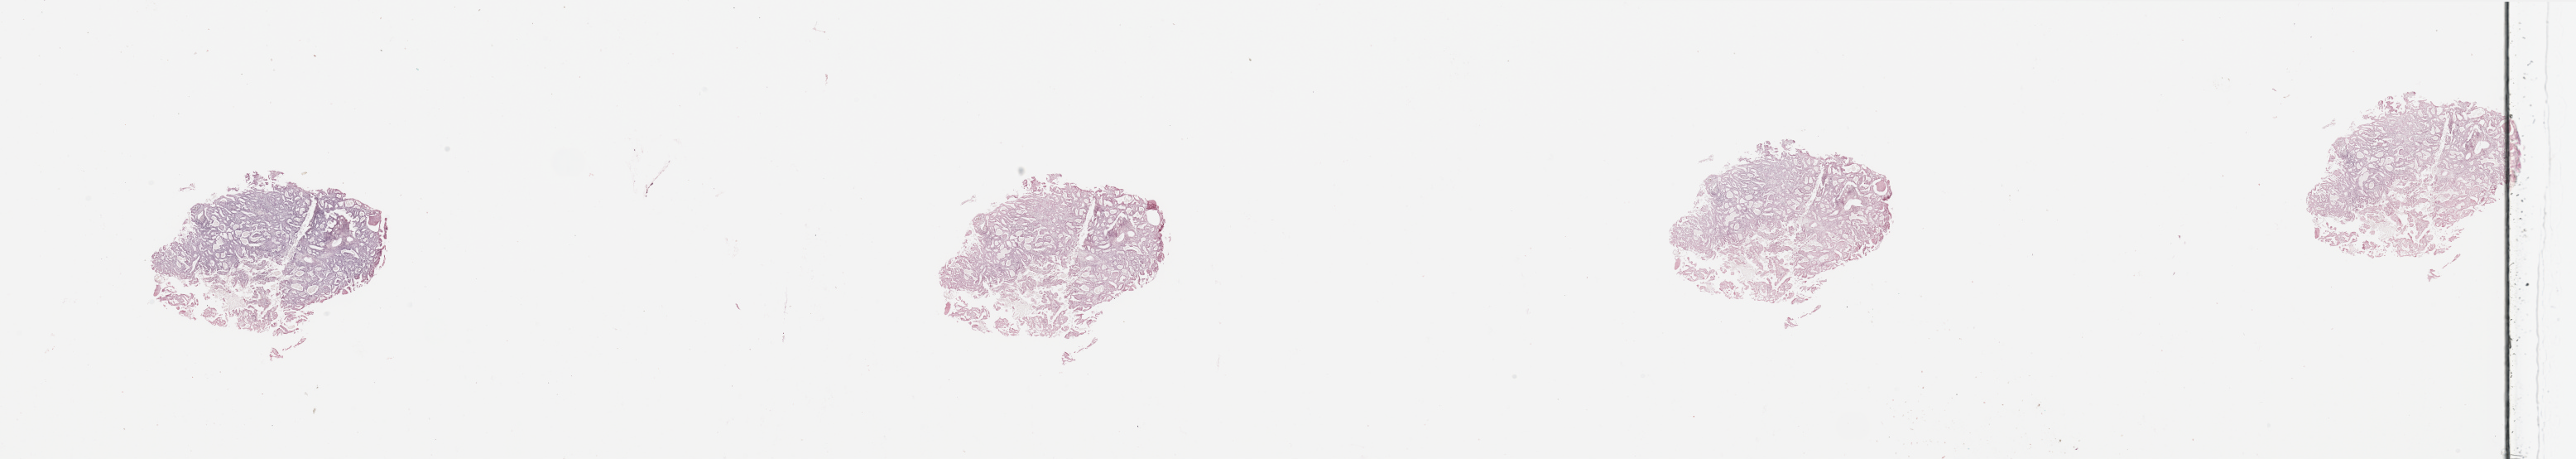
H&E whole-slide image — shown as a low-resolution overview of the whole scanned area (about 49.2 x 8.8 mm). Tumour tissue sample, sampled site: uterus. Patient: female, age 58 years. Histologic grade: G1 (well differentiated). Pathologist review of this section (percent, as recorded): tumour nuclei 85%, necrosis 2%.
• histologic diagnosis: Endometrioid adenocarcinoma, NOS
• primary tumour site (as recorded): posterior endometrium
• AJCC pathologic stage: III